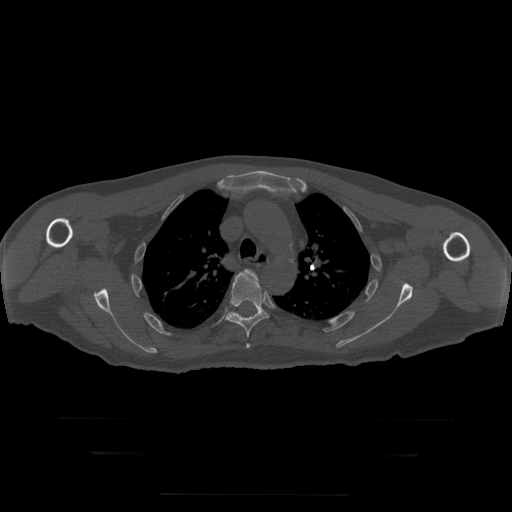
CT including the spine, one axial slice; 120 kVp; bone window (W 1800 / L 400 HU); 512 × 512 image matrix, field of view 510 × 510 mm. Patient age 73 years. Case-level facts recorded for this patient, not image findings: primary cancer: prostate.
Outlined on this slice (semi-automatically segmented with operator editing):
- T4 vertebra: box from (x=241, y=269) to (x=258, y=279) px
- T5 vertebra: (x=225, y=273)–(x=269, y=349)
- T6 vertebra: (x=231, y=312)–(x=241, y=317)